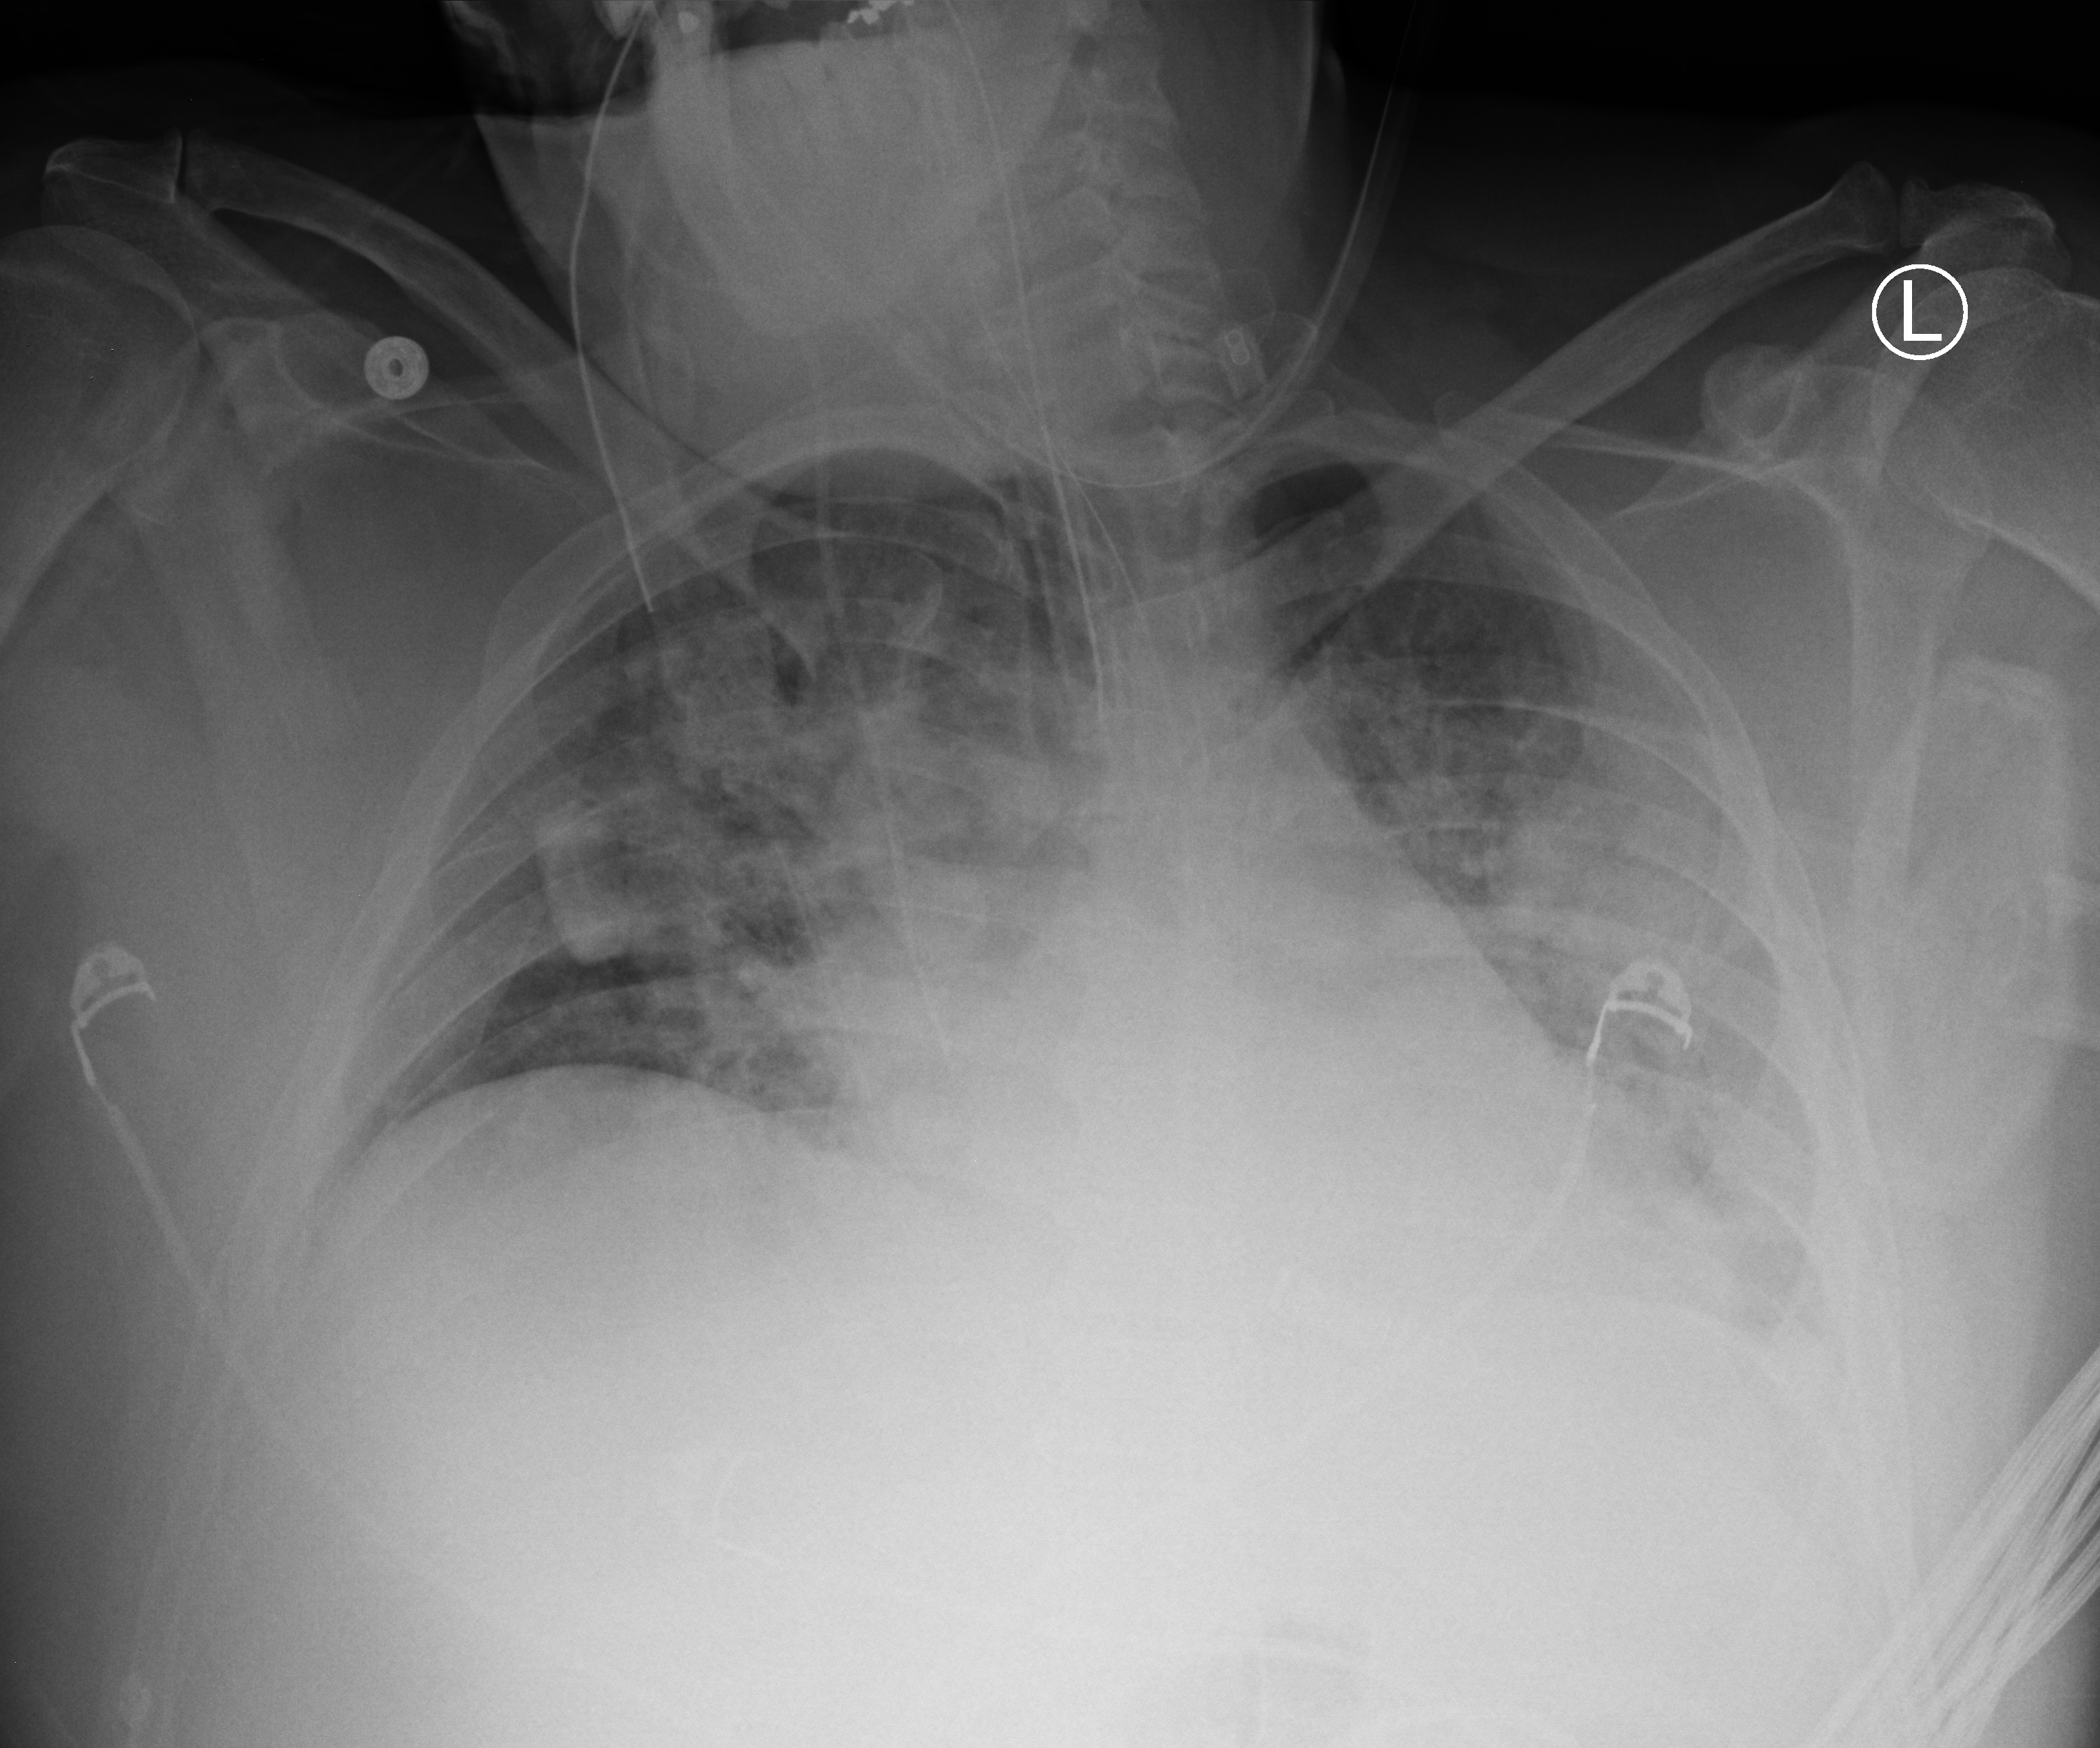
Bedside chest radiograph (computed radiography). Patient hospitalised with COVID-19; male, aged 18–59 years.
Admission-level facts for this patient (not findings on this image; timing relative to this image not recorded): mechanically ventilated during this hospital stay: yes; COPD (admission record): no.